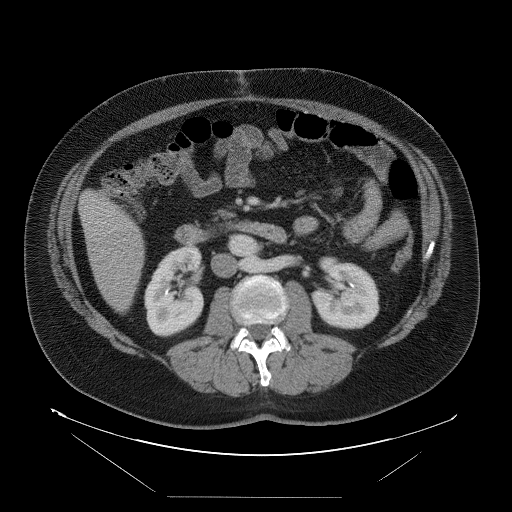
Contrast-enhanced abdominal CT, one axial slice; position 27 of 114 along the scan axis; intravenous contrast given; soft-tissue window (W 400 / L 40 HU); 512 × 512 image matrix, field of view 500 × 500 mm. Male patient, age 61 years. Case-level facts recorded for this patient, not image findings: diagnosis: colorectal cancer liver metastases, imaged before liver resection; multiple liver metastases: no; largest metastasis: 6.5 cm; disease in both lobes: yes.
Structures marked on this image (expert manual segmentation):
- liver: bounding box (x1, y1, x2, y2) in pixels: (81, 191, 145, 312)